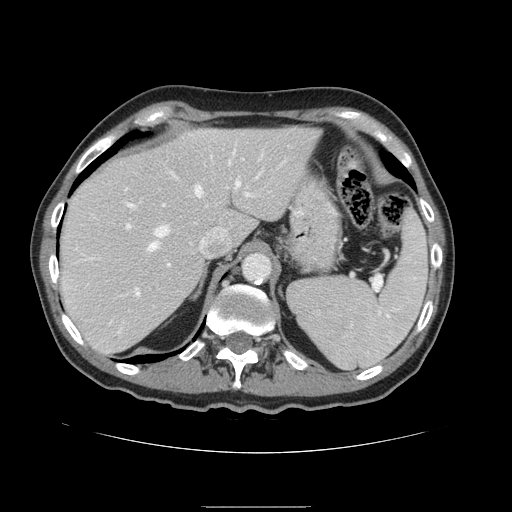
Contrast-enhanced abdominal CT, one axial slice. Position 113 of 168 along the scan axis. 120 kVp. Intravenous contrast given. Soft-tissue window (W 400 / L 40 HU). 2.5 mm slice thickness. 512 × 512 image matrix, field of view 386 × 386 mm. Male patient, age 74 years. Case-level facts recorded for this patient, not image findings: diagnosis: colorectal cancer liver metastases, imaged before liver resection; multiple liver metastases: no; largest metastasis: 14.5 cm.
Outlined on this slice (expert manual segmentation):
- hepatic veins: box from (x=129, y=172) to (x=262, y=250) px
- liver: (x=60, y=127)–(x=320, y=354)
- planned liver remnant (the part of the liver to remain after resection): (x=60, y=127)–(x=320, y=354)
- portal vein (with intrahepatic branches): (x=121, y=192)–(x=253, y=297)